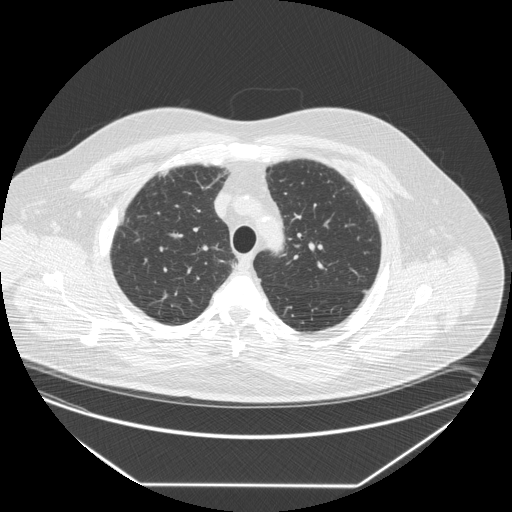
Low-dose screening chest CT, one axial slice. Slice 209 of 258 in the series (ordered by position). Lung window (W 1500 / L -600 HU). 2.5 mm slice thickness. 512 × 512 image matrix.
Annotated regions visible in this slice (outlined manually by an expert reader):
- lesion 1 (tumor, upper lobe of right lung): bounding box (x1, y1, x2, y2) in pixels: (232, 263, 237, 268)